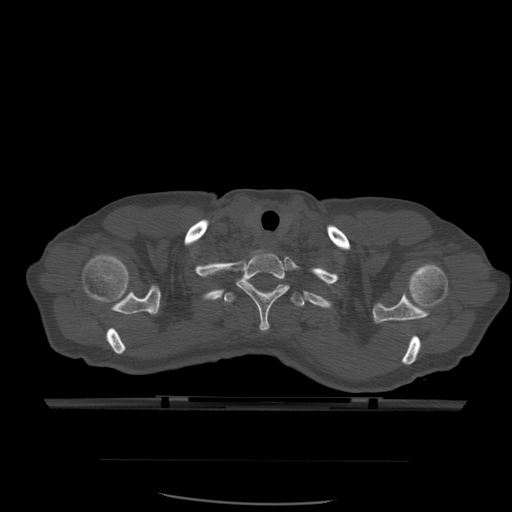
CT including the spine, one axial slice; slice 468 of 574 in the series (ordered by position); bone window (W 1800 / L 400 HU); 1.25 mm slice thickness; 512 × 512 image matrix, field of view 392 × 392 mm. Patient age 48 years. Case-level facts recorded for this patient, not image findings: primary cancer: lung.
Outlined on this slice (semi-automatic segmentation, software-assisted and operator-edited):
- T1 vertebra: box from (x=236, y=250) to (x=290, y=332) px
- T2 vertebra: (x=224, y=281)–(x=305, y=308)